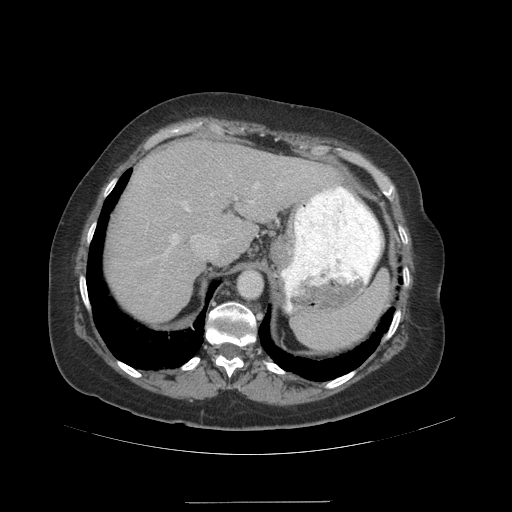
Contrast-enhanced abdominal CT (liver protocol), one axial slice; reconstruction kernel STANDARD; 140 kVp; soft-tissue window (W 400 / L 40 HU); 2.5 mm slice thickness; 512 × 512 image matrix. From the clinical record (not read from this slice): diagnosis: hepatocellular carcinoma (patient treated with transarterial chemoembolisation; whether this scan precedes or follows treatment is not stated here); TNM stage (as recorded): Stage-IVA; Child-Pugh class: A; tumour nodularity: multinodular.
Annotated regions visible in this slice (semi-automatic segmentation, software-assisted and operator-edited):
- abdominal aorta: box from (x=238, y=270) to (x=261, y=299) px
- liver parenchyma outside the tumour (the mass and vessels are separate outlines, so this box may not span the whole liver): (x=108, y=140)–(x=336, y=320)
- liver vessels: (x=164, y=175)–(x=282, y=256)